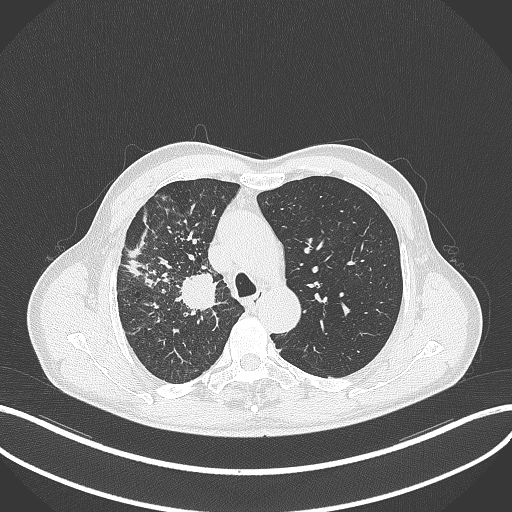
Chest CT, one axial slice. Position 347 of 490 along the scan axis. Reconstruction kernel B70f. 120 kVp. Lung window (W 1500 / L -600 HU). 1 mm slice thickness. 512 × 512 image matrix. Male patient, age 69 years. From the clinical record (not read from this slice): clinical TNM (as recorded): T2a N0 M0.
Structures marked on this image (bounding box drawn by a radiologist):
- lung tumour (recorded histology: adenocarcinoma): bounding box [x1, y1, x2, y2] px = [178, 271, 220, 312]